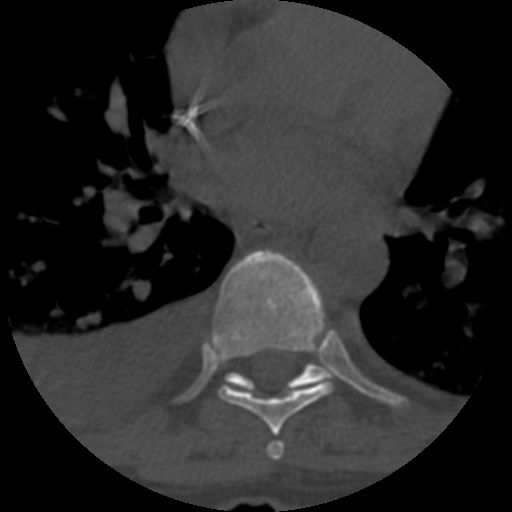
CT including the spine, one axial slice. One of 3 acquisitions stored at this slice position. Bone window (W 1800 / L 400 HU). 1.25 mm slice thickness. 512 × 512 image matrix, field of view 160 × 160 mm. Patient age 55 years. From the clinical record (not read from this slice): primary cancer: colon; vertebrae with lytic lesions (as recorded): T12, L1, L5.
Structures marked on this image (semi-automatic segmentation, software-assisted and operator-edited):
- T6 vertebra: bounding box <267,441,285,460> (left, top, right, bottom; pixels)
- T7 vertebra: <213,250,334,436>
- T8 vertebra: <225,363,330,393>